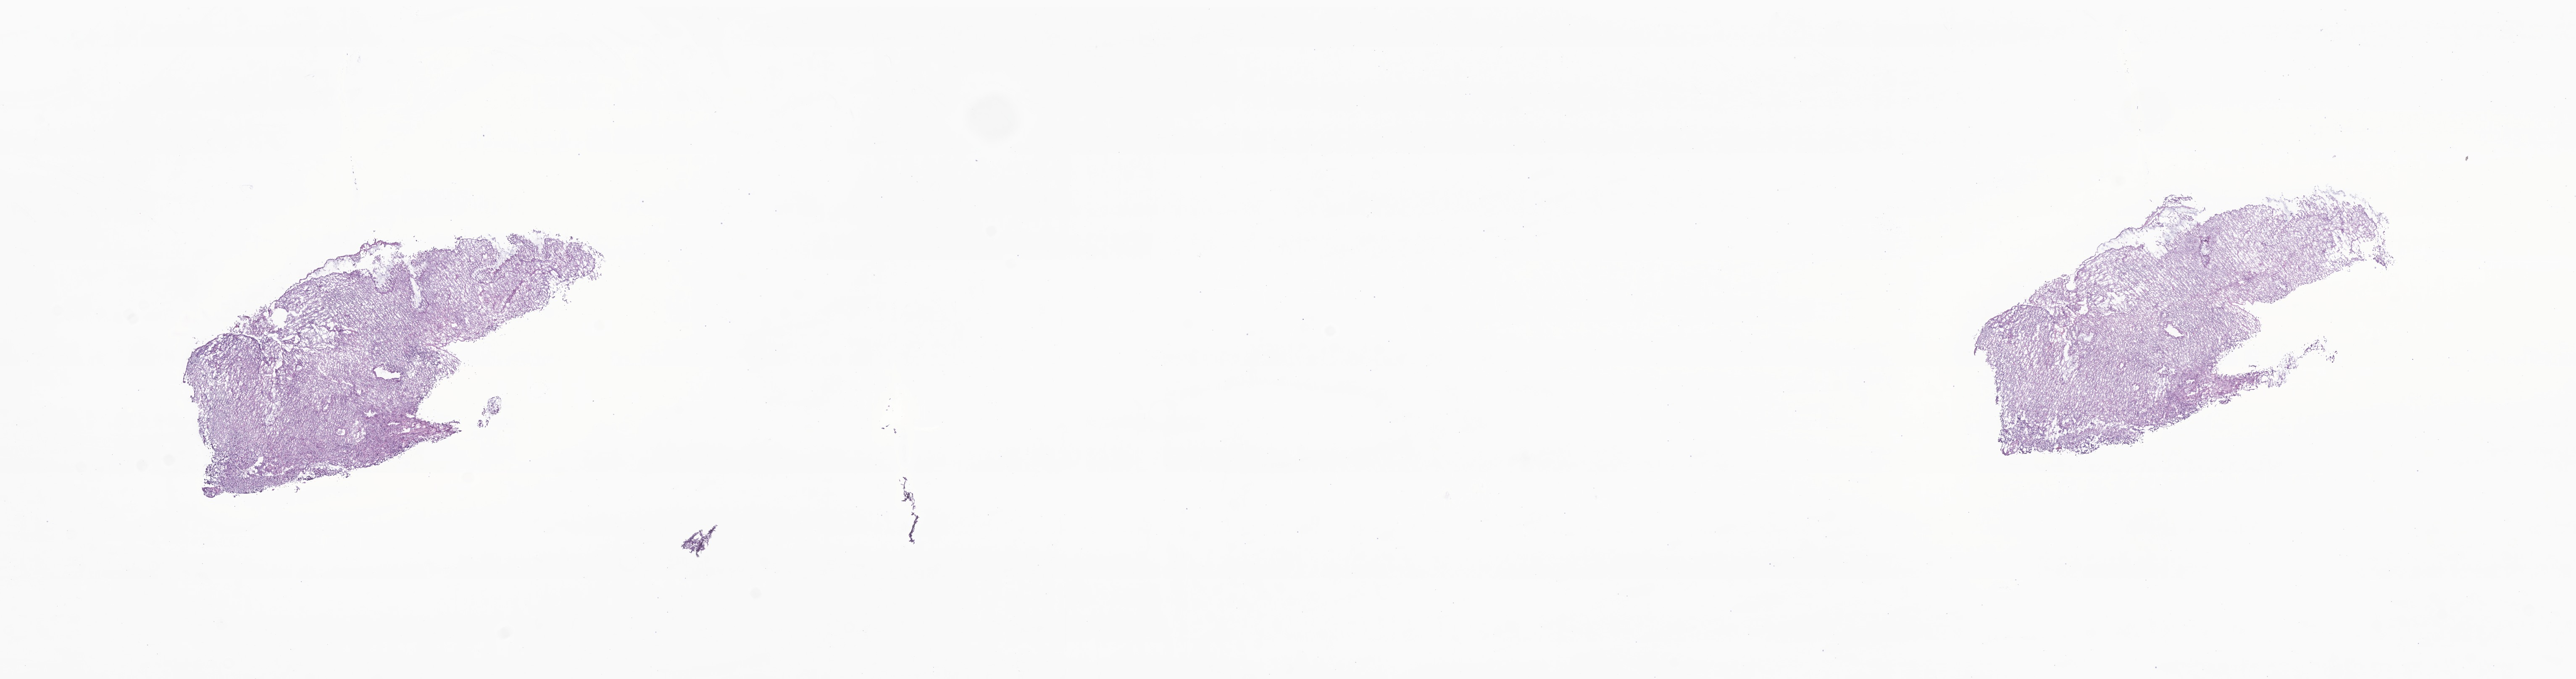
Whole-slide image, hematoxylin and eosin (H&E) stain of tumor tissue from the nasopharynx, low-resolution overview of the scanned area, about 25.8 x 6.8 mm. Frozen section. Male patient, age 169 months.
Recorded diagnosis: Carcinoma, NOS.